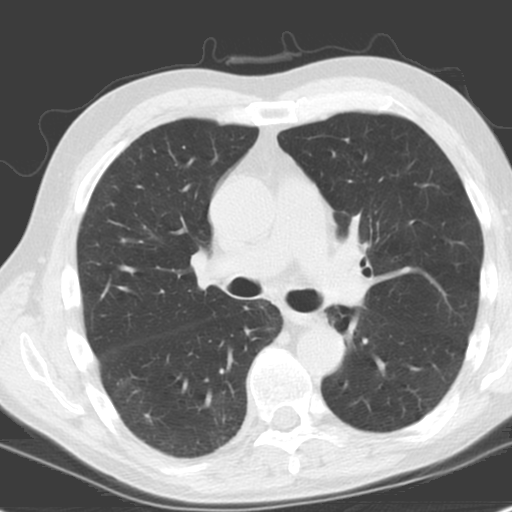
Chest CT (low-dose screening protocol), one axial image. Baseline screening round. Lung window (W 1500 / L -600 HU). 3.2 mm slice thickness. Standard (soft-tissue) reconstruction kernel (C). 120 kVp. 512 × 512 image matrix, field of view 321 × 321 mm. Male participant, aged 61 years at enrolment. Former smoker at enrolment.
Lesion marked by an expert reader, bounding box (x1, y1, x2, y2) in pixels: (308, 301, 352, 341). Screening reader's record for this exam: no non-calcified nodule ≥4 mm recorded. Official screen result: negative screen, minor abnormalities not suspicious for lung cancer. Lung cancer was diagnosed 1146 days after this screen (after the third annual screen): squamous cell carcinoma, NOS, left upper lobe, left lower lobe, well differentiated (G1), stage IIB (AJCC 6th edition), 100 mm at pathology.